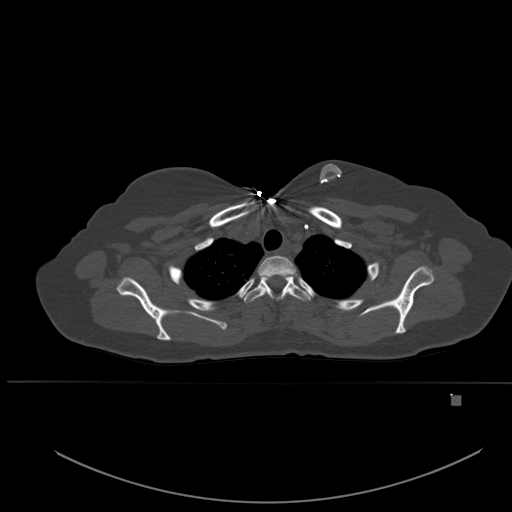
CT including the spine, one axial slice. Position 410 of 651 along the scan axis. Bone window (W 1800 / L 400 HU). 1.5 mm slice thickness. 512 × 512 image matrix, field of view 443 × 443 mm. Female patient, age 49 years. From the clinical record (not read from this slice): primary cancer: breast.
Outlined on this slice (semi-automatically segmented with operator editing):
- T1 vertebra: bounding box (x1, y1, x2, y2) in pixels: (257, 255, 296, 279)
- T2 vertebra: (243, 276, 311, 303)